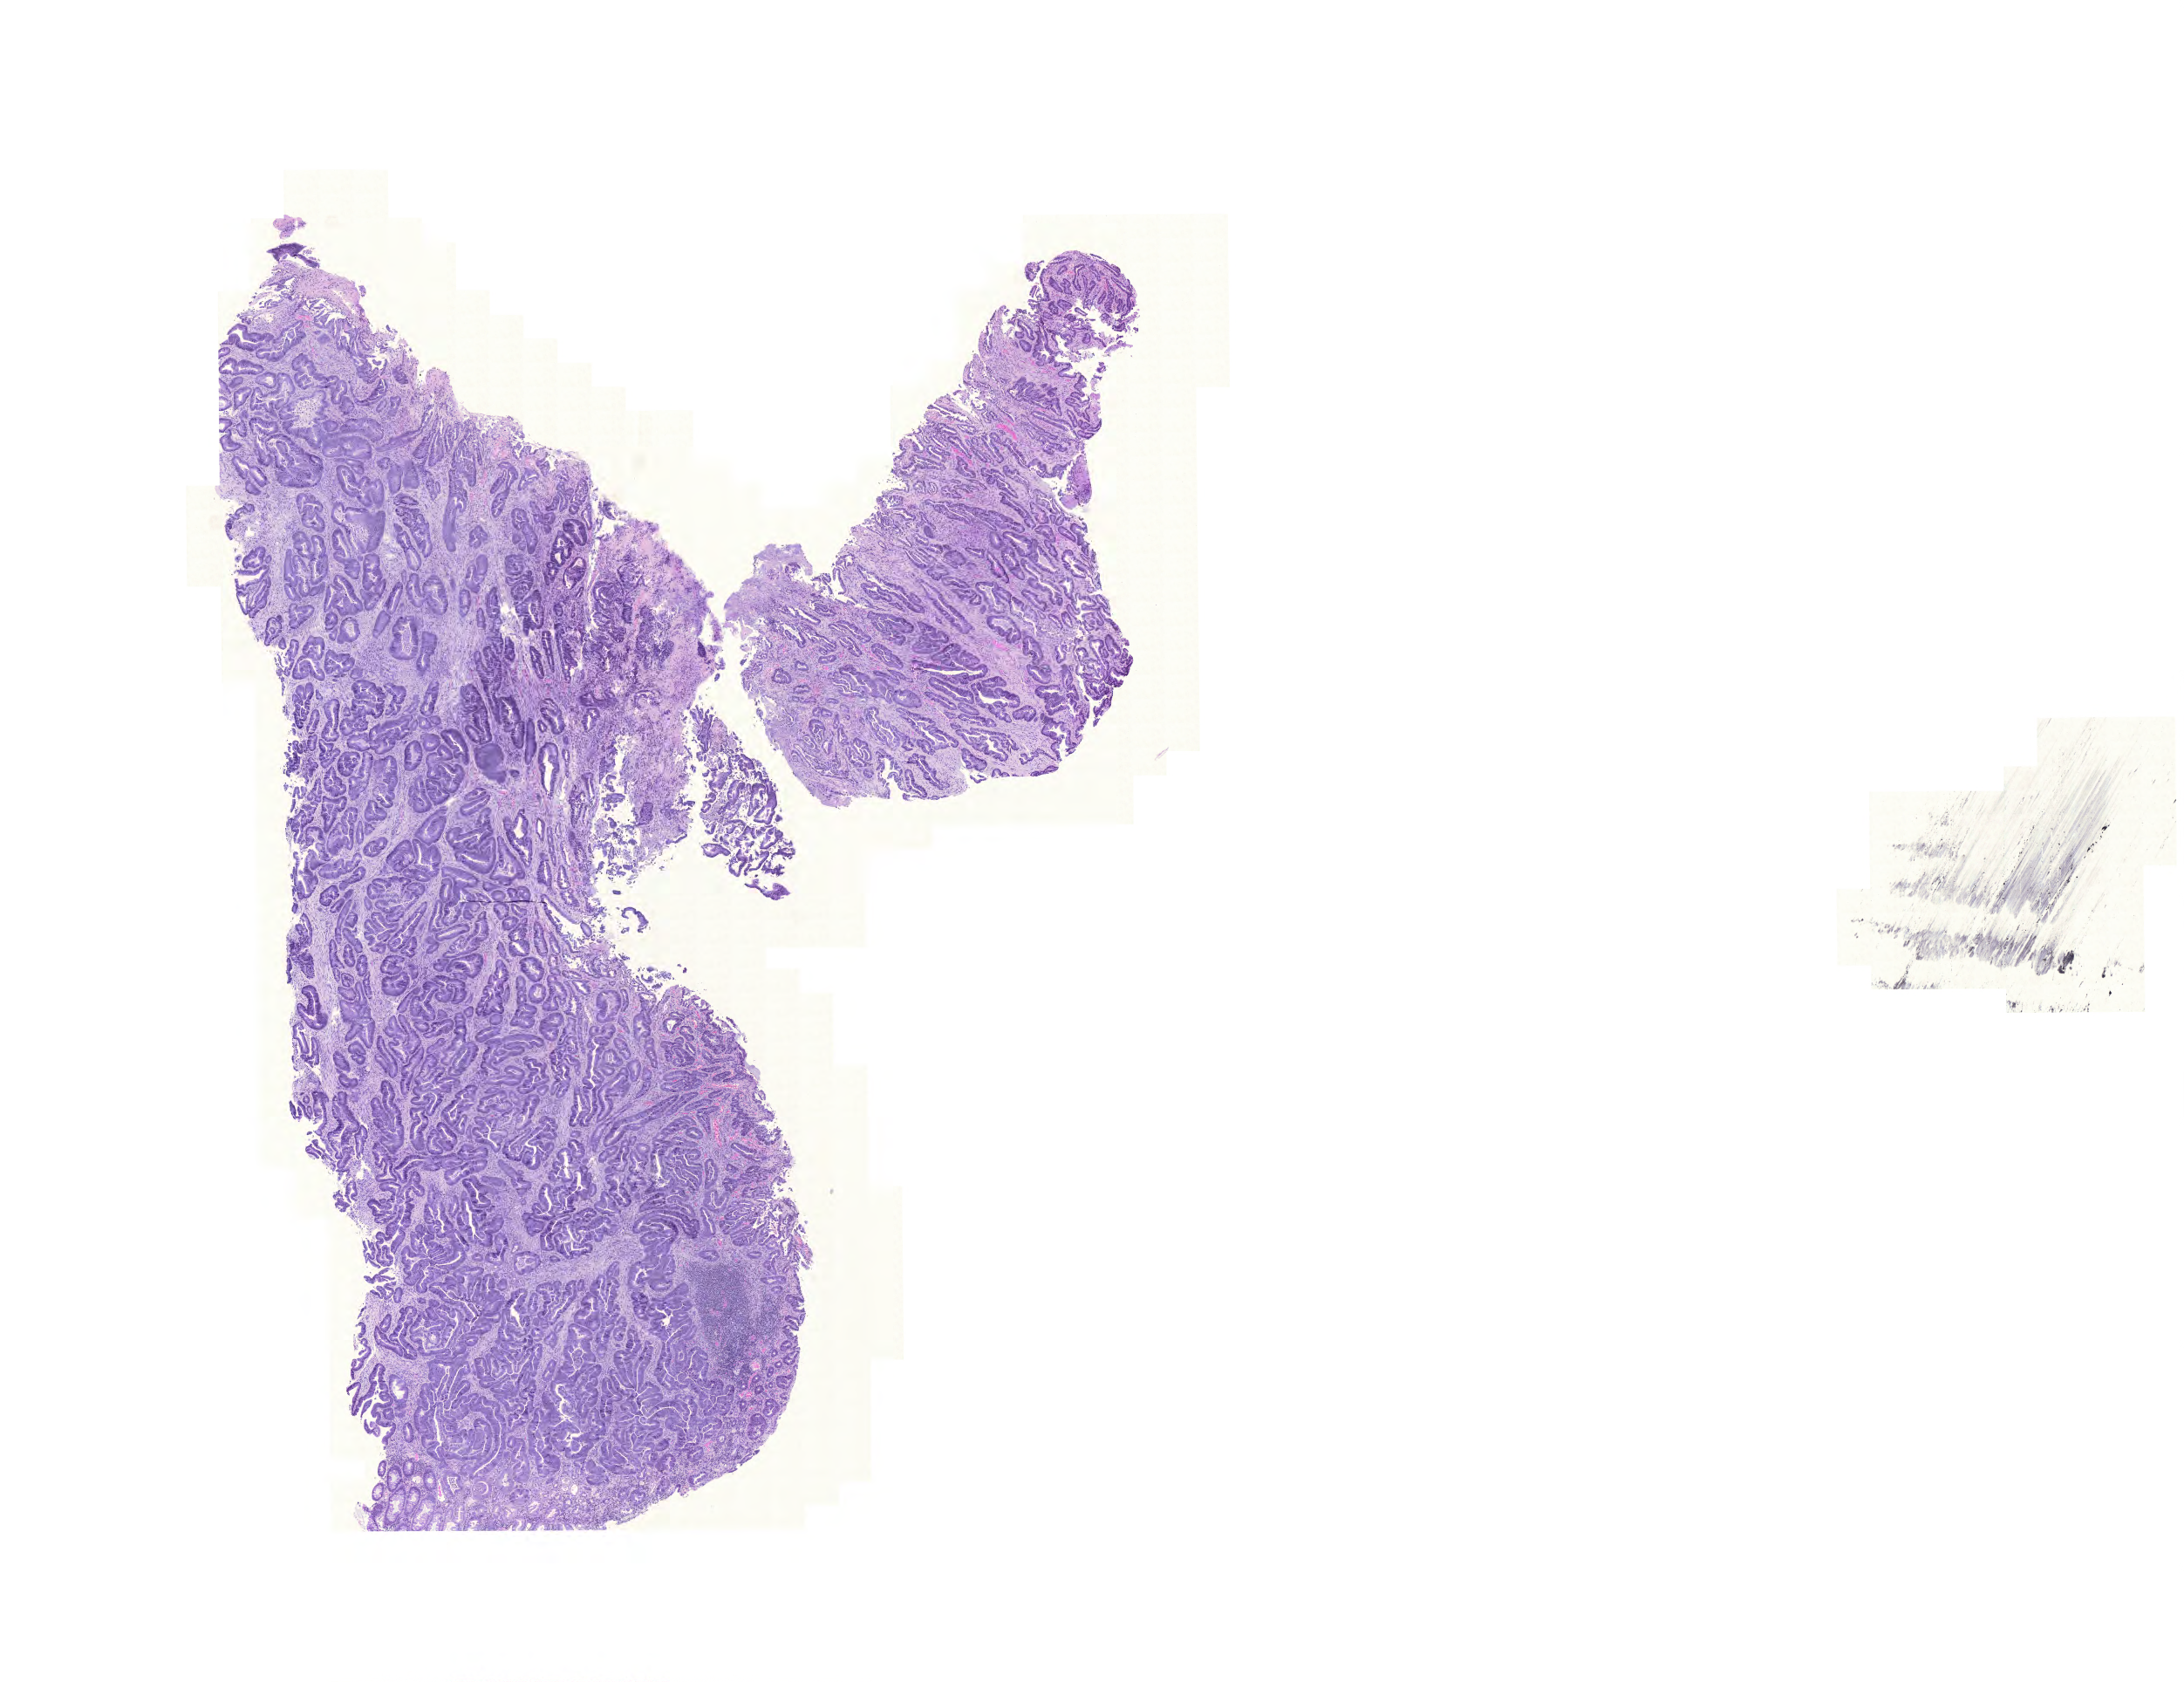
Hematoxylin and eosin (H&E) stained whole-slide image — shown as a low-resolution overview of the whole scanned area (about 18.6 x 14.3 mm, acquisition: 20x scan); formalin-fixed paraffin-embedded (FFPE) diagnostic section; primary tumour sample from the colon. Female, age 82 years at initial diagnosis.
Pathologic diagnosis: Adenocarcinoma, NOS (sigmoid colon). AJCC pathologic stage: IIA.